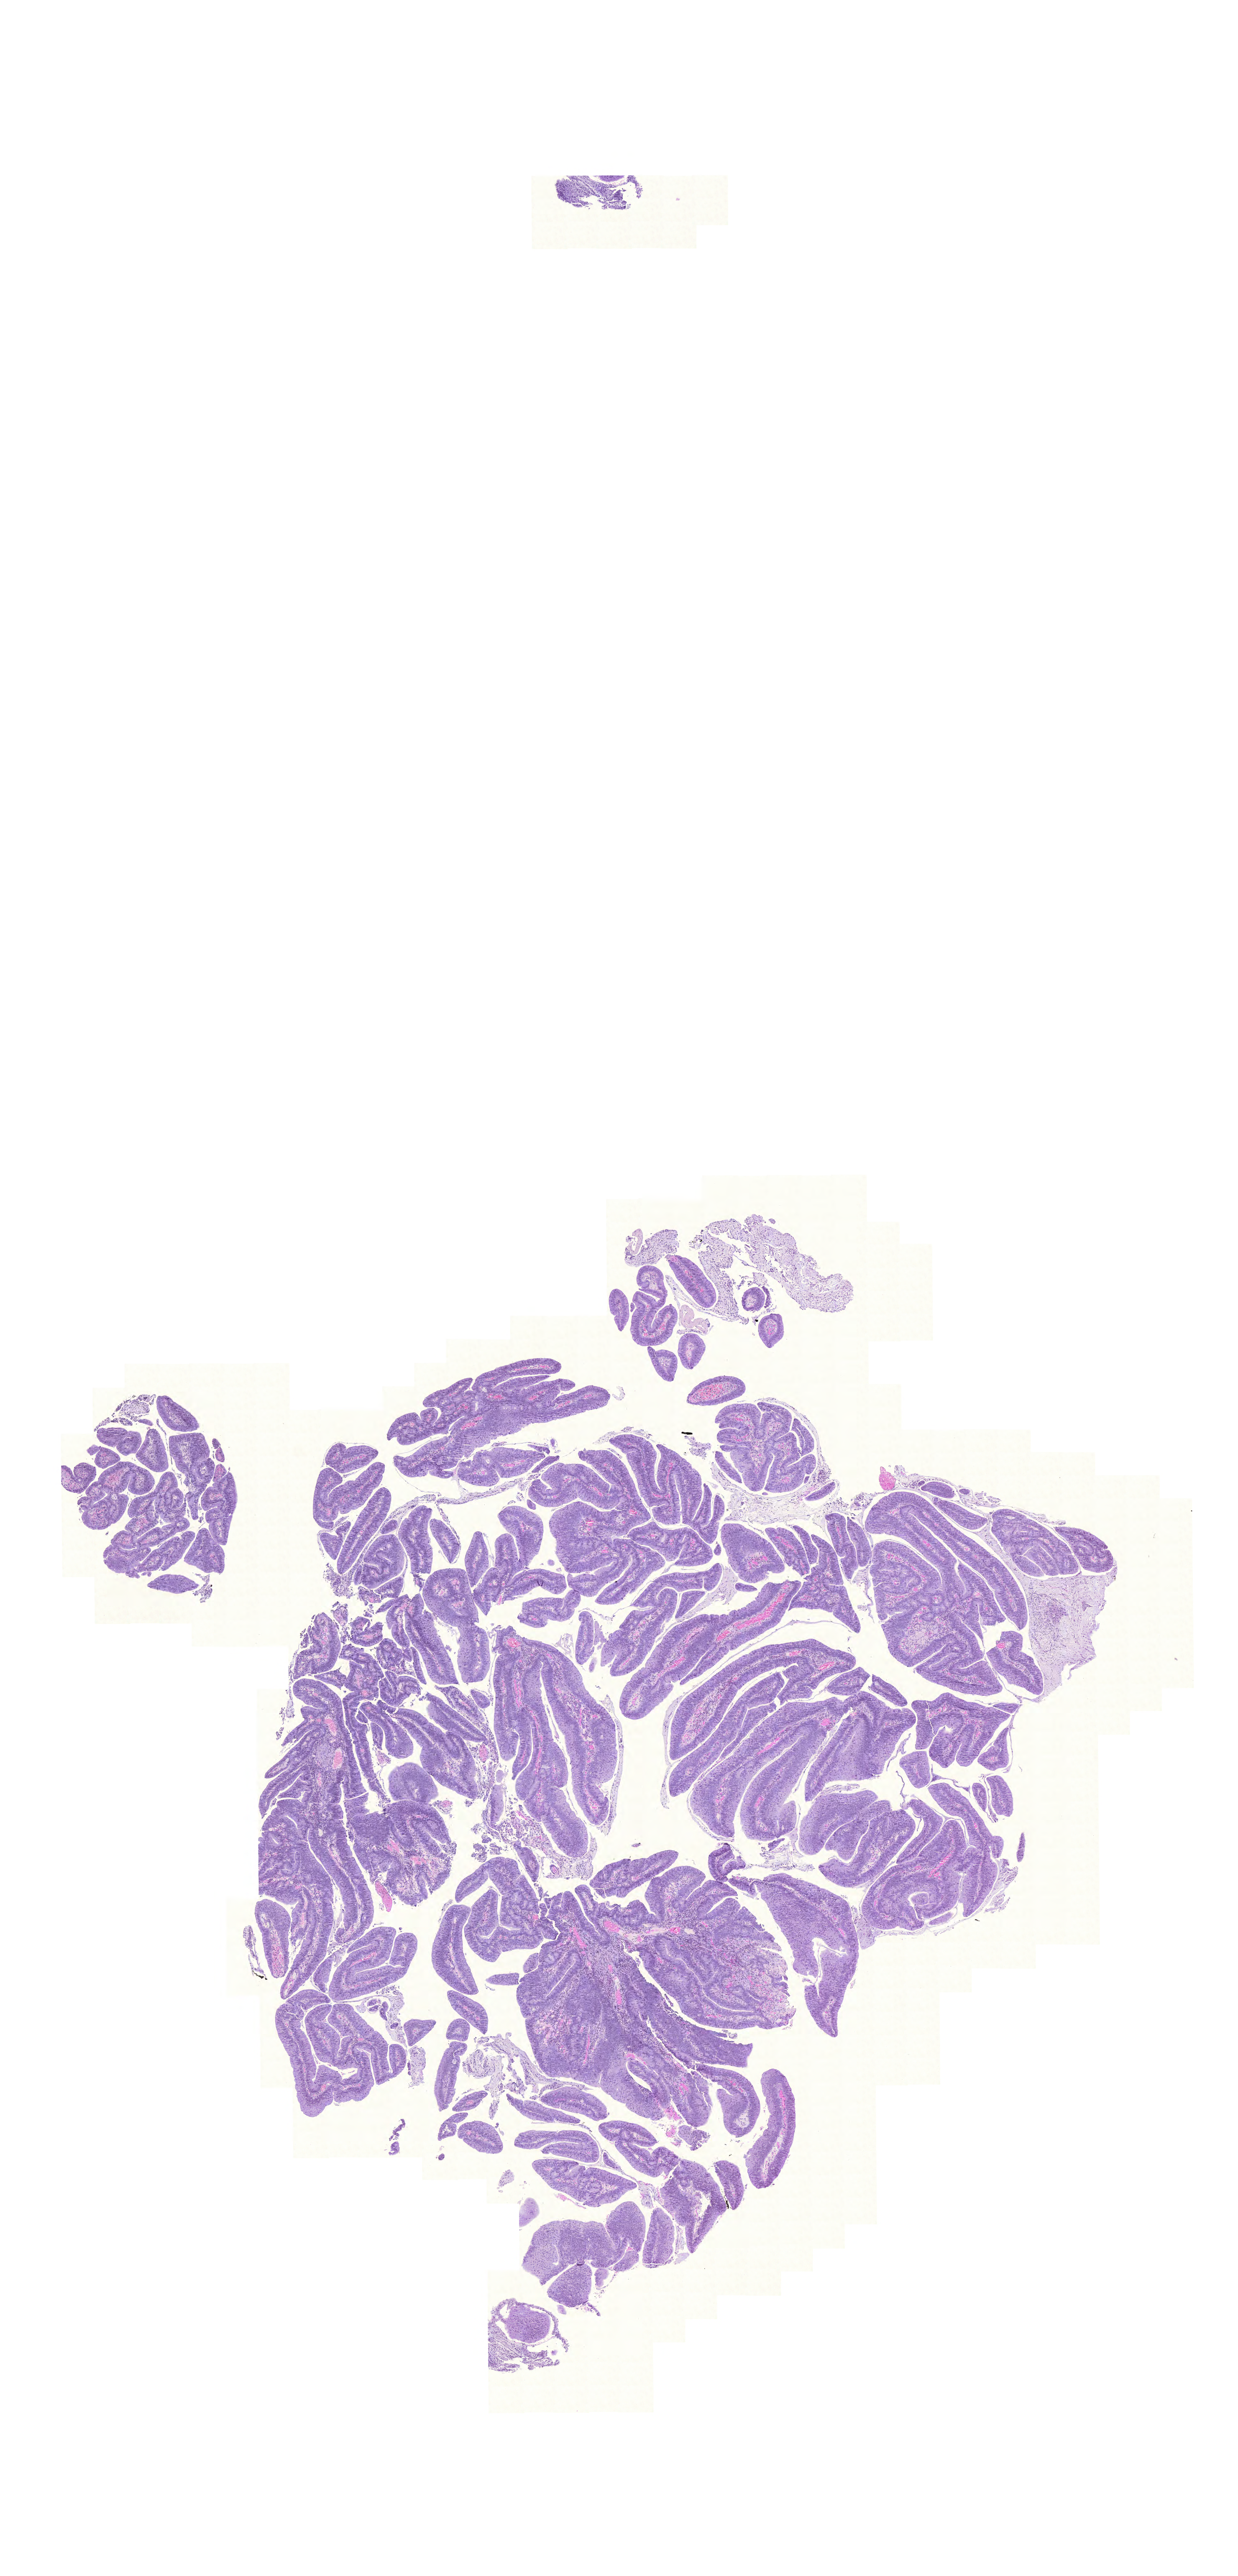
Whole-slide histology image, H&E-stained — a low-resolution overview of the entire scanned area, about 11.0 x 22.9 mm (acquisition: 20x scan), formalin-fixed paraffin-embedded (FFPE) diagnostic section, rectum, primary tumour sample. Male patient; age at initial diagnosis 77 years.
* diagnosis: Mucinous adenocarcinoma (rectosigmoid junction)
* AJCC pathologic stage: IIA
* lymph nodes positive (case pathology): 0 of 25 examined